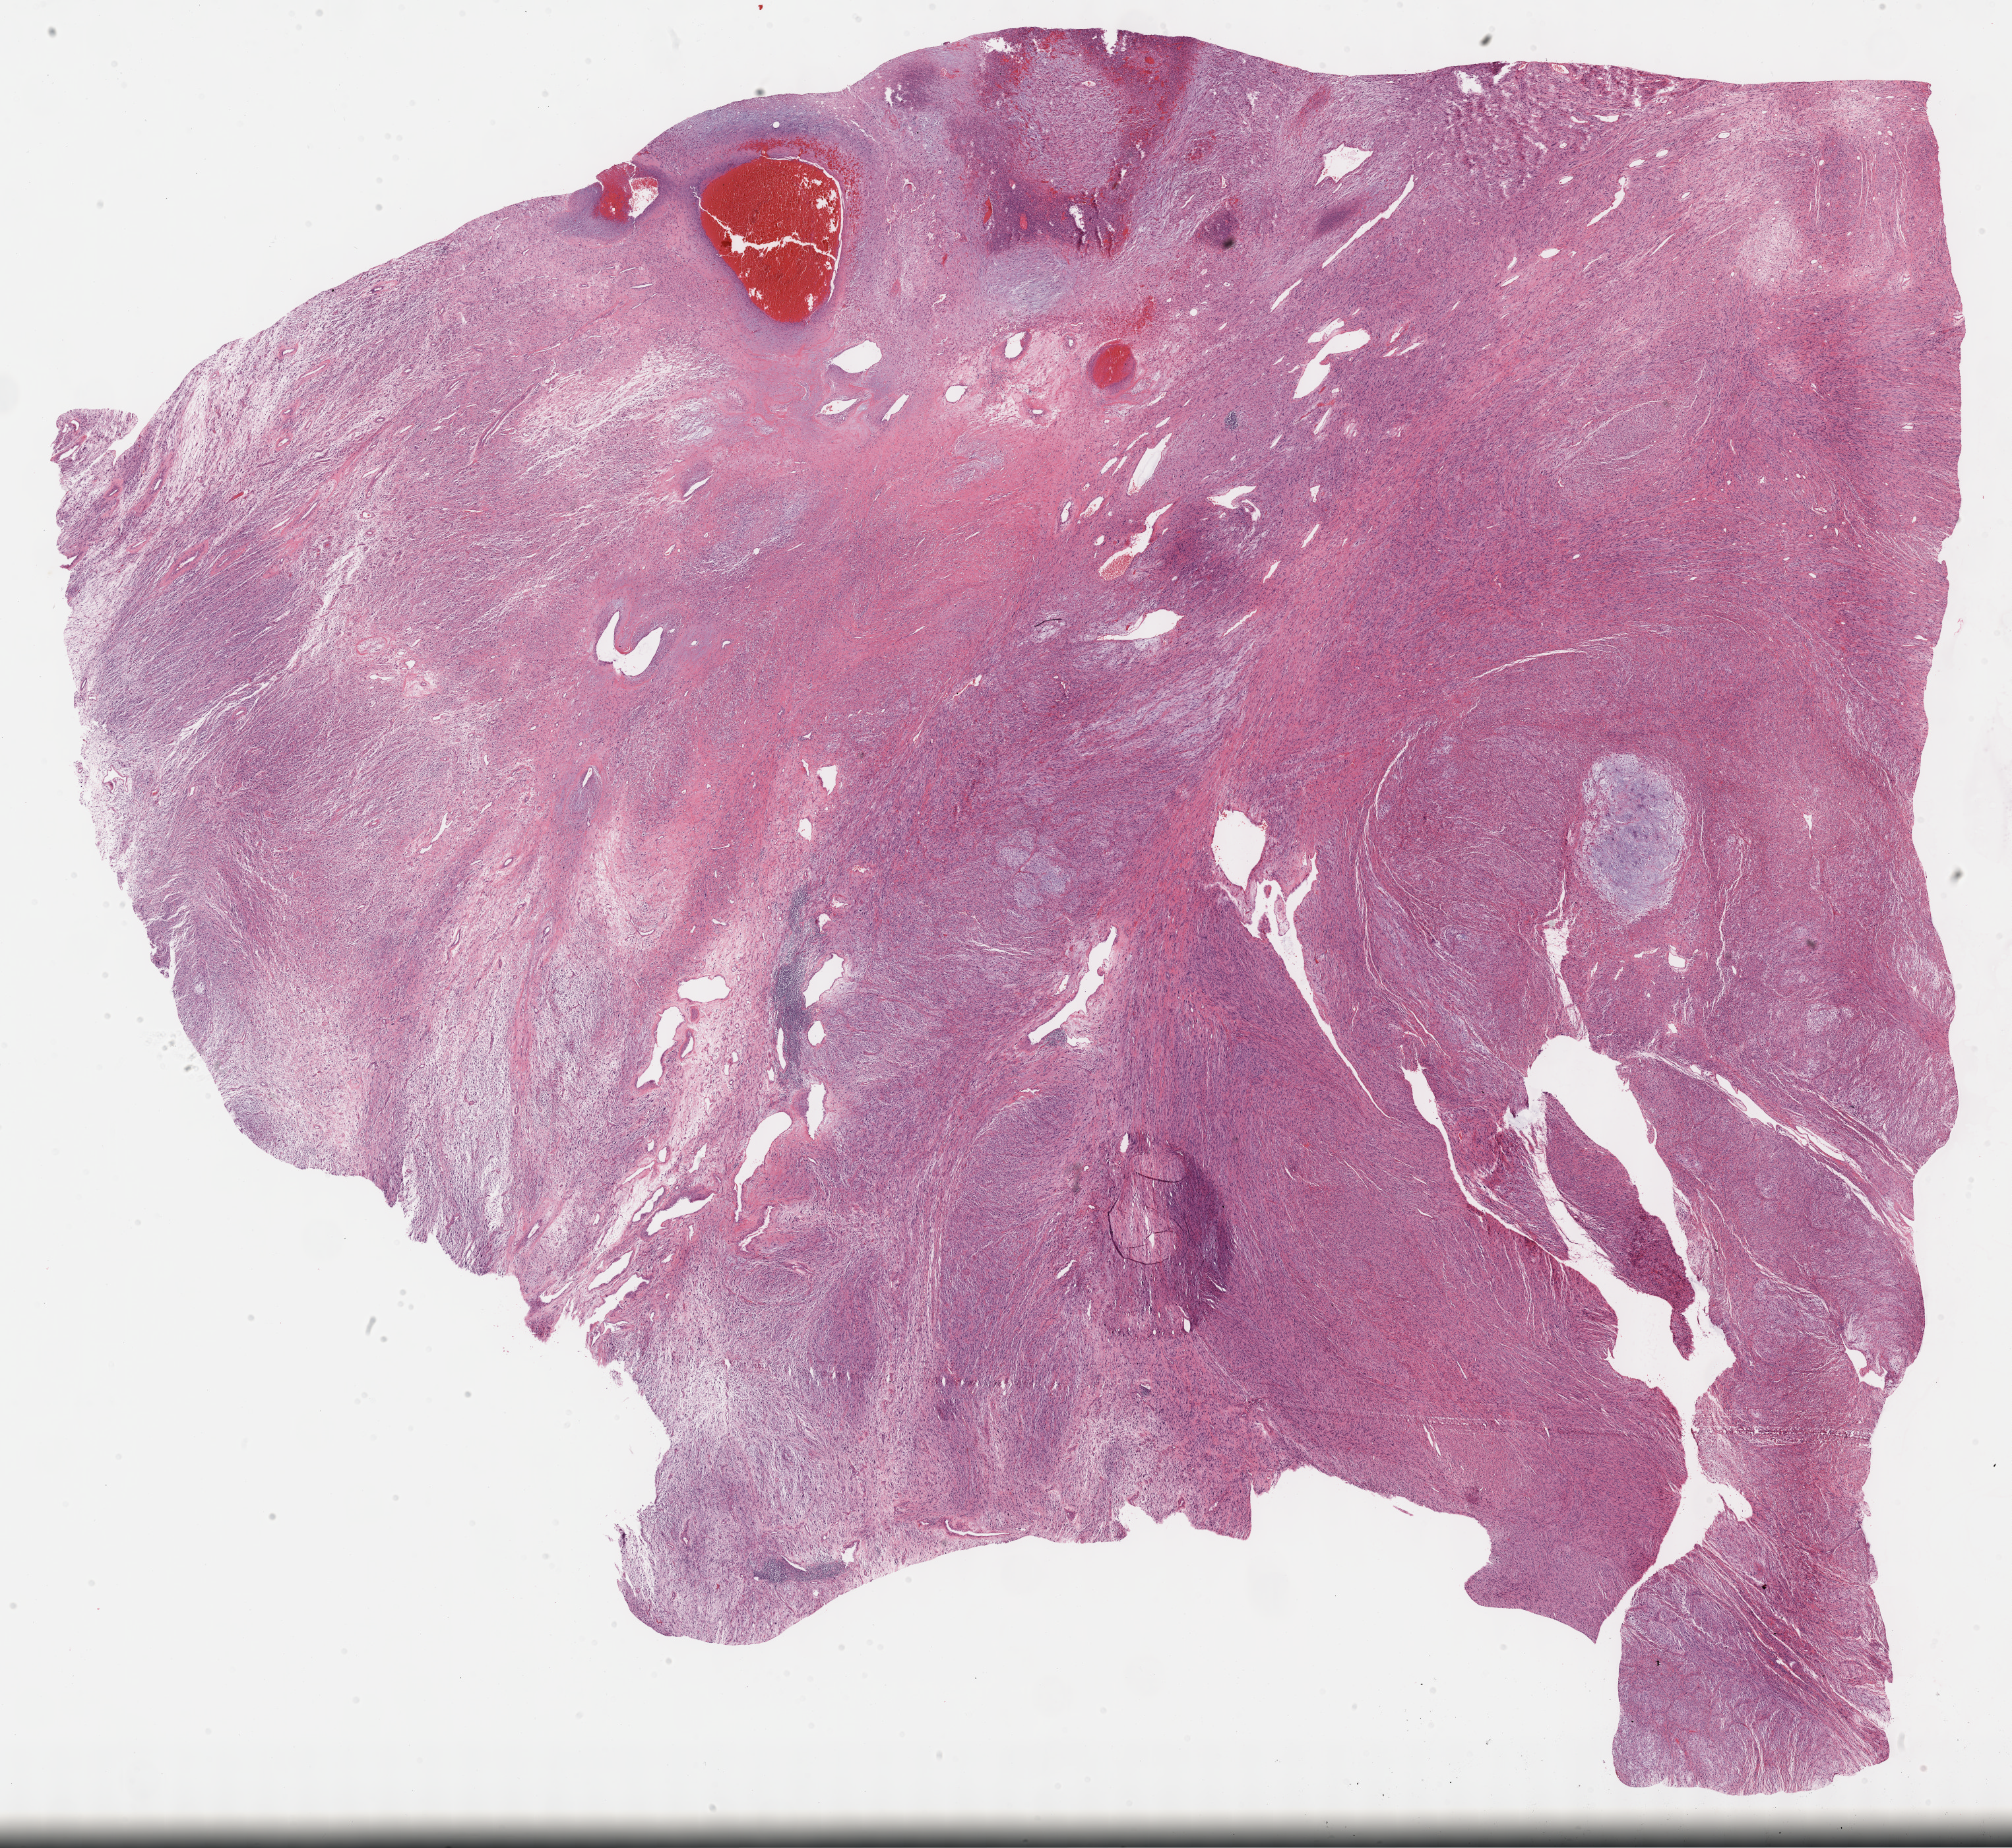
Digitized Hematoxylin and eosin (H&E) stained tissue section (whole slide), a low-resolution overview of the entire scanned area, about 24.7 x 22.7 mm (from a 40x scan), formalin-fixed paraffin-embedded (FFPE) diagnostic section, connective, subcutaneous and other soft tissues, primary tumour sample. Male patient; age at initial diagnosis 59 years.
Diagnosis: Fibromyxosarcoma.